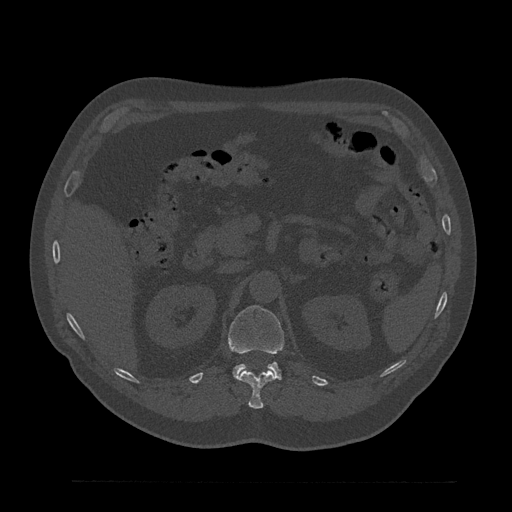
CT including the spine, one axial slice. Position 195 of 797 along the scan axis. Reconstruction kernel Br40s/3. Bone window (W 1800 / L 400 HU). 0.5 mm slice thickness. 512 × 512 image matrix, field of view 430 × 430 mm. Patient: male, 61 years. Case-level facts recorded for this patient, not image findings: primary cancer: prostate.
Outlined on this slice (semi-automatic segmentation, software-assisted and operator-edited):
- L1 vertebra: box from (x=228, y=306) to (x=284, y=379) px
- T12 vertebra: (x=237, y=370)–(x=276, y=409)